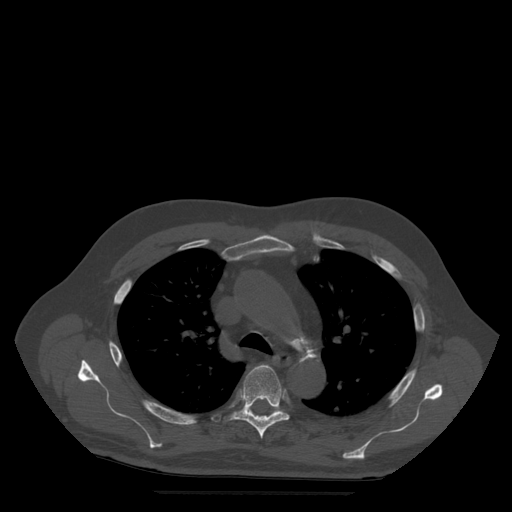
CT including the spine, one axial slice. Position 373 of 522 along the scan axis. Bone window (W 1800 / L 400 HU). 512 × 512 image matrix. Patient age 72 years. From the clinical record (not read from this slice): primary cancer: prostate.
Outlined on this slice (semi-automatic segmentation, software-assisted and operator-edited):
- T5 vertebra: box from (x=225, y=365) to (x=289, y=439) px